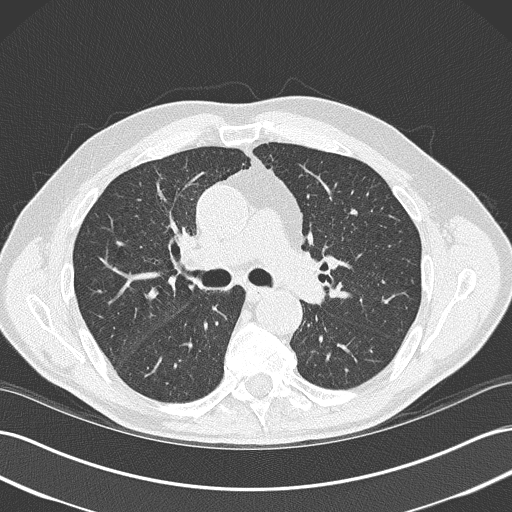
Low-dose screening chest CT, axial slice; first (baseline) screen; lung window (W 1500 / L -600 HU); 2 mm slice thickness; lung (sharp) reconstruction kernel (B50f); 120 kVp; slice 99 of 171 in the series; 512 × 512 image matrix, field of view 360 × 360 mm. Male, age 73 years at enrolment. Current smoker at enrolment.
• Expert-annotated lung lesion, bounding box (x1, y1, x2, y2) in pixels: (334, 198, 374, 232).
• The screening reader recorded 2 non-calcified nodules or masses ≥4 mm on this exam; which of them this box marks is not recorded.
• Official screen result: positive, change unspecified: nodule(s) >= 4 mm or enlarging nodule(s), mass(es), or other non-specific abnormalities suspicious for lung cancer.
• Later outcome: lung cancer diagnosed 400 days after this screen (after the second annual screen) — small cell carcinoma, NOS, left upper lobe, stage IIIB (AJCC 6th edition), 19 mm at pathology.